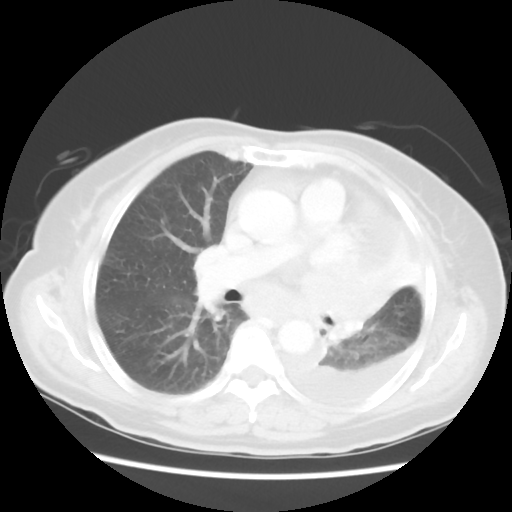
Chest CT, one axial slice; position 31 of 52 along the scan axis; reconstruction kernel STANDARD; 120 kVp; lung window (W 1500 / L -600 HU); 5 mm slice thickness; 512 × 512 image matrix, field of view 336 × 336 mm. Female patient, age 72 years. Case-level facts recorded for this patient, not image findings: clinical TNM (as recorded): T4 N3 M1b.
Structures marked on this image (bounding box drawn by a radiologist):
- lung tumour (recorded histology: large cell carcinoma): bounding box <295,256,392,350> (left, top, right, bottom; pixels)